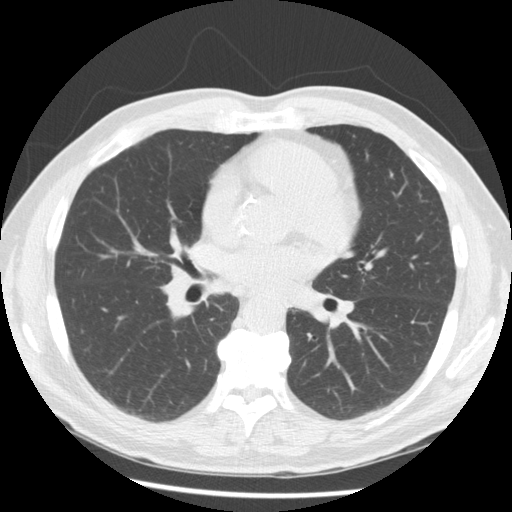
Axial slice from a low-dose chest CT screening exam, baseline screening round, lung window (W 1500 / L -600 HU), 2.5 mm slice thickness, 512 × 512 image matrix. Male, age 62 years at enrolment.
Expert-annotated lung lesion, bounding box <156,249,218,309> (left, top, right, bottom; pixels). No non-calcified nodule or mass ≥4 mm was recorded by the screening reader at this exam.